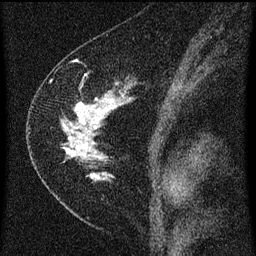
Breast MRI (dynamic contrast-enhanced), one sagittal slice. Position 37 of 60 along the scan axis. Dynamic contrast-enhanced series, image 2 of 3 at this slice position (ordered by acquisition). 1.5 T. TE 4.2 ms, TR 8 ms. 2 mm slice thickness. 256 × 256 image matrix, field of view 180 × 180 mm. Female patient, age 47 years.
Outlined on this slice (semi-automatic segmentation, software-assisted and operator-edited):
- analysis volume of interest (the breast-tissue region the enhancement analysis was run in; not a lesion): box from (x=38, y=76) to (x=132, y=191) px
- tumour enhancement mask (voxels above the 70 % enhancement threshold inside the analysis volume of interest): (x=62, y=98)–(x=121, y=179)